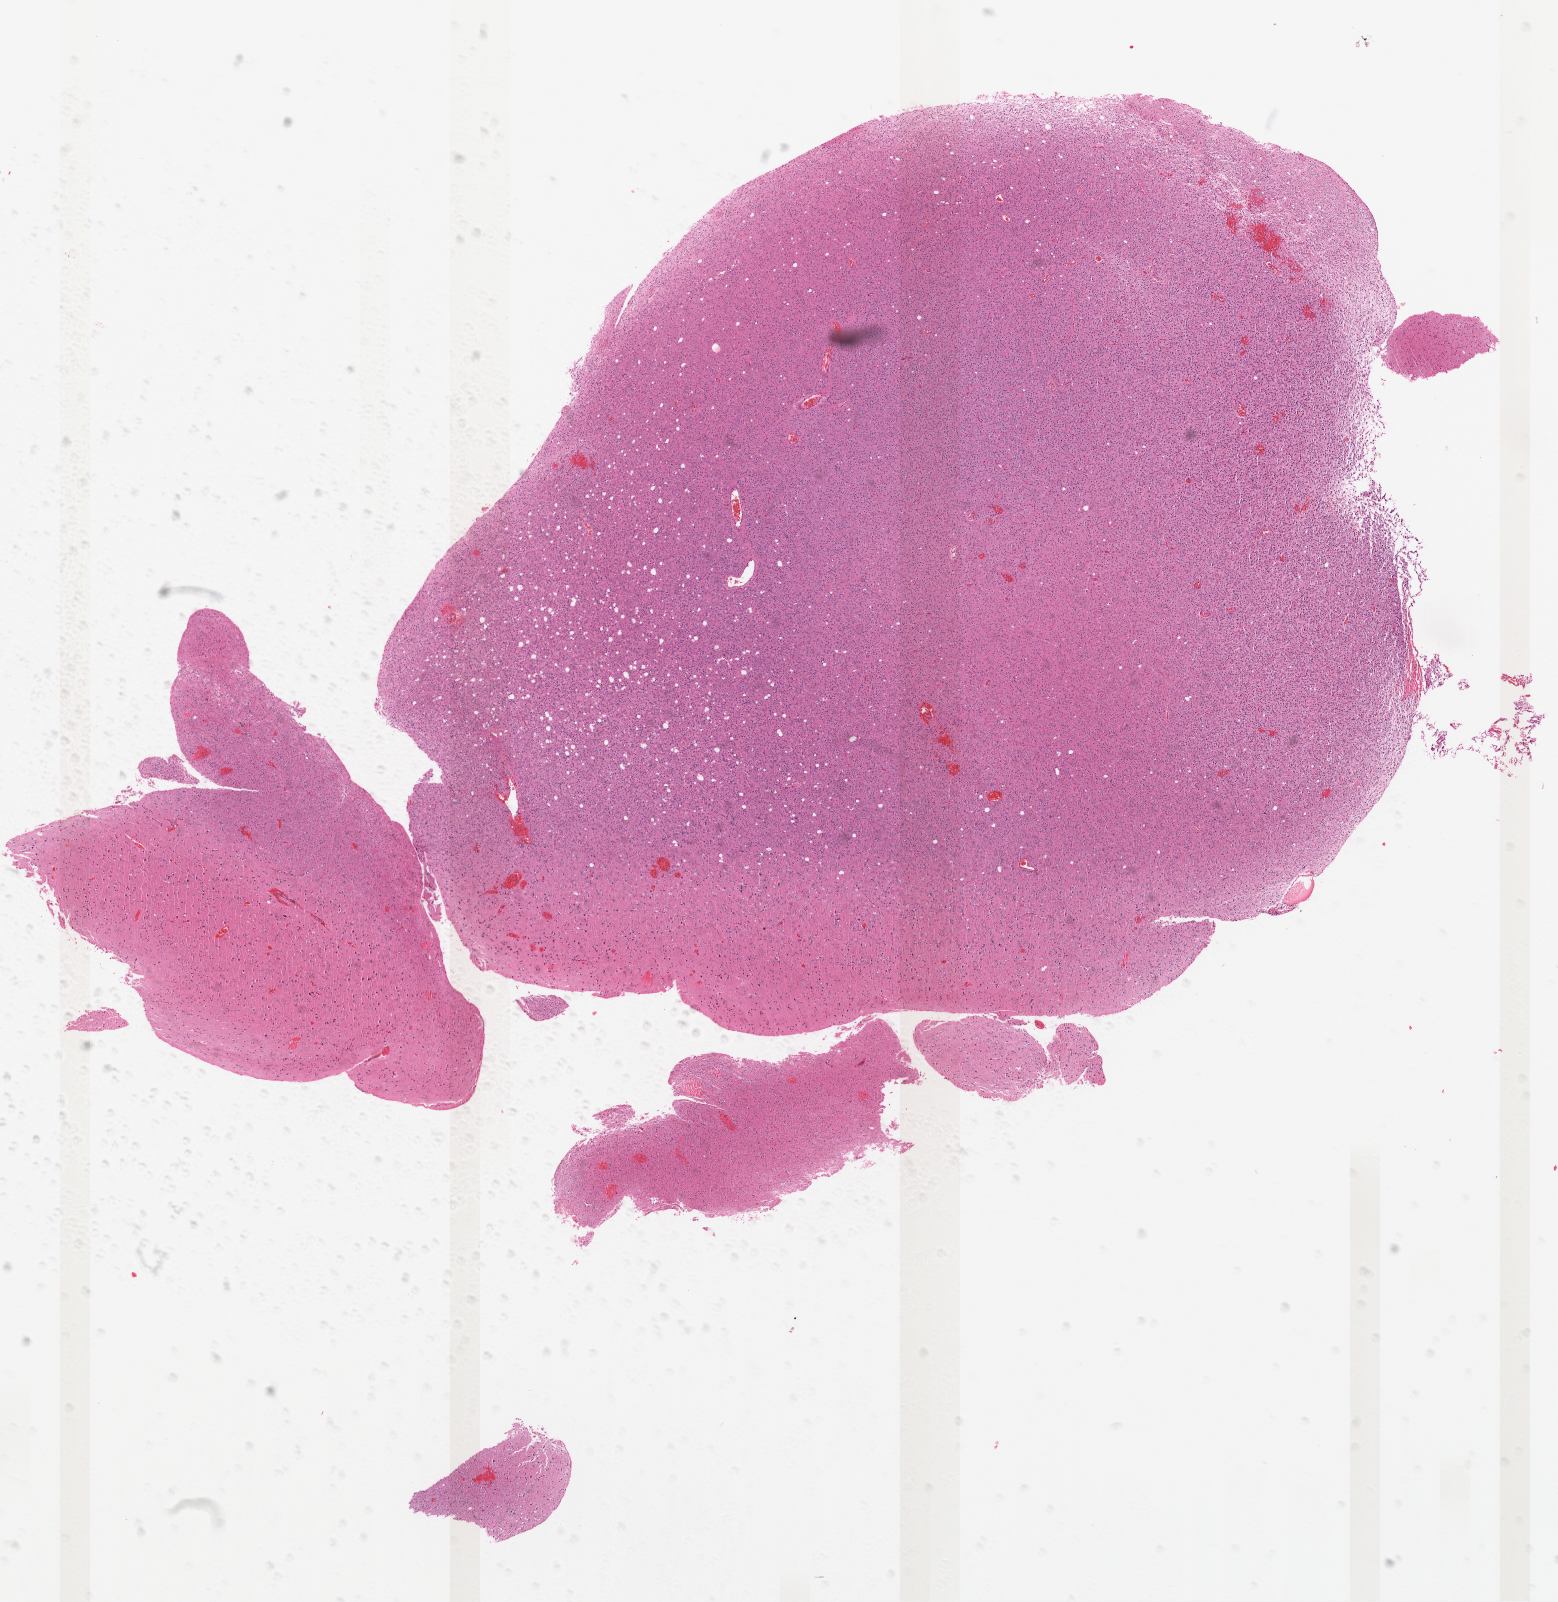
Digitized H&E tissue section (whole slide) — whole scanned area (about 12.6 x 12.9 mm, slide scanned at 40x) shown as a low-resolution overview; formalin-fixed paraffin-embedded (FFPE) diagnostic section; primary tumour sample from the brain. Male patient; age at initial diagnosis 31 years.
Histologic diagnosis: Mixed glioma (cerebrum).